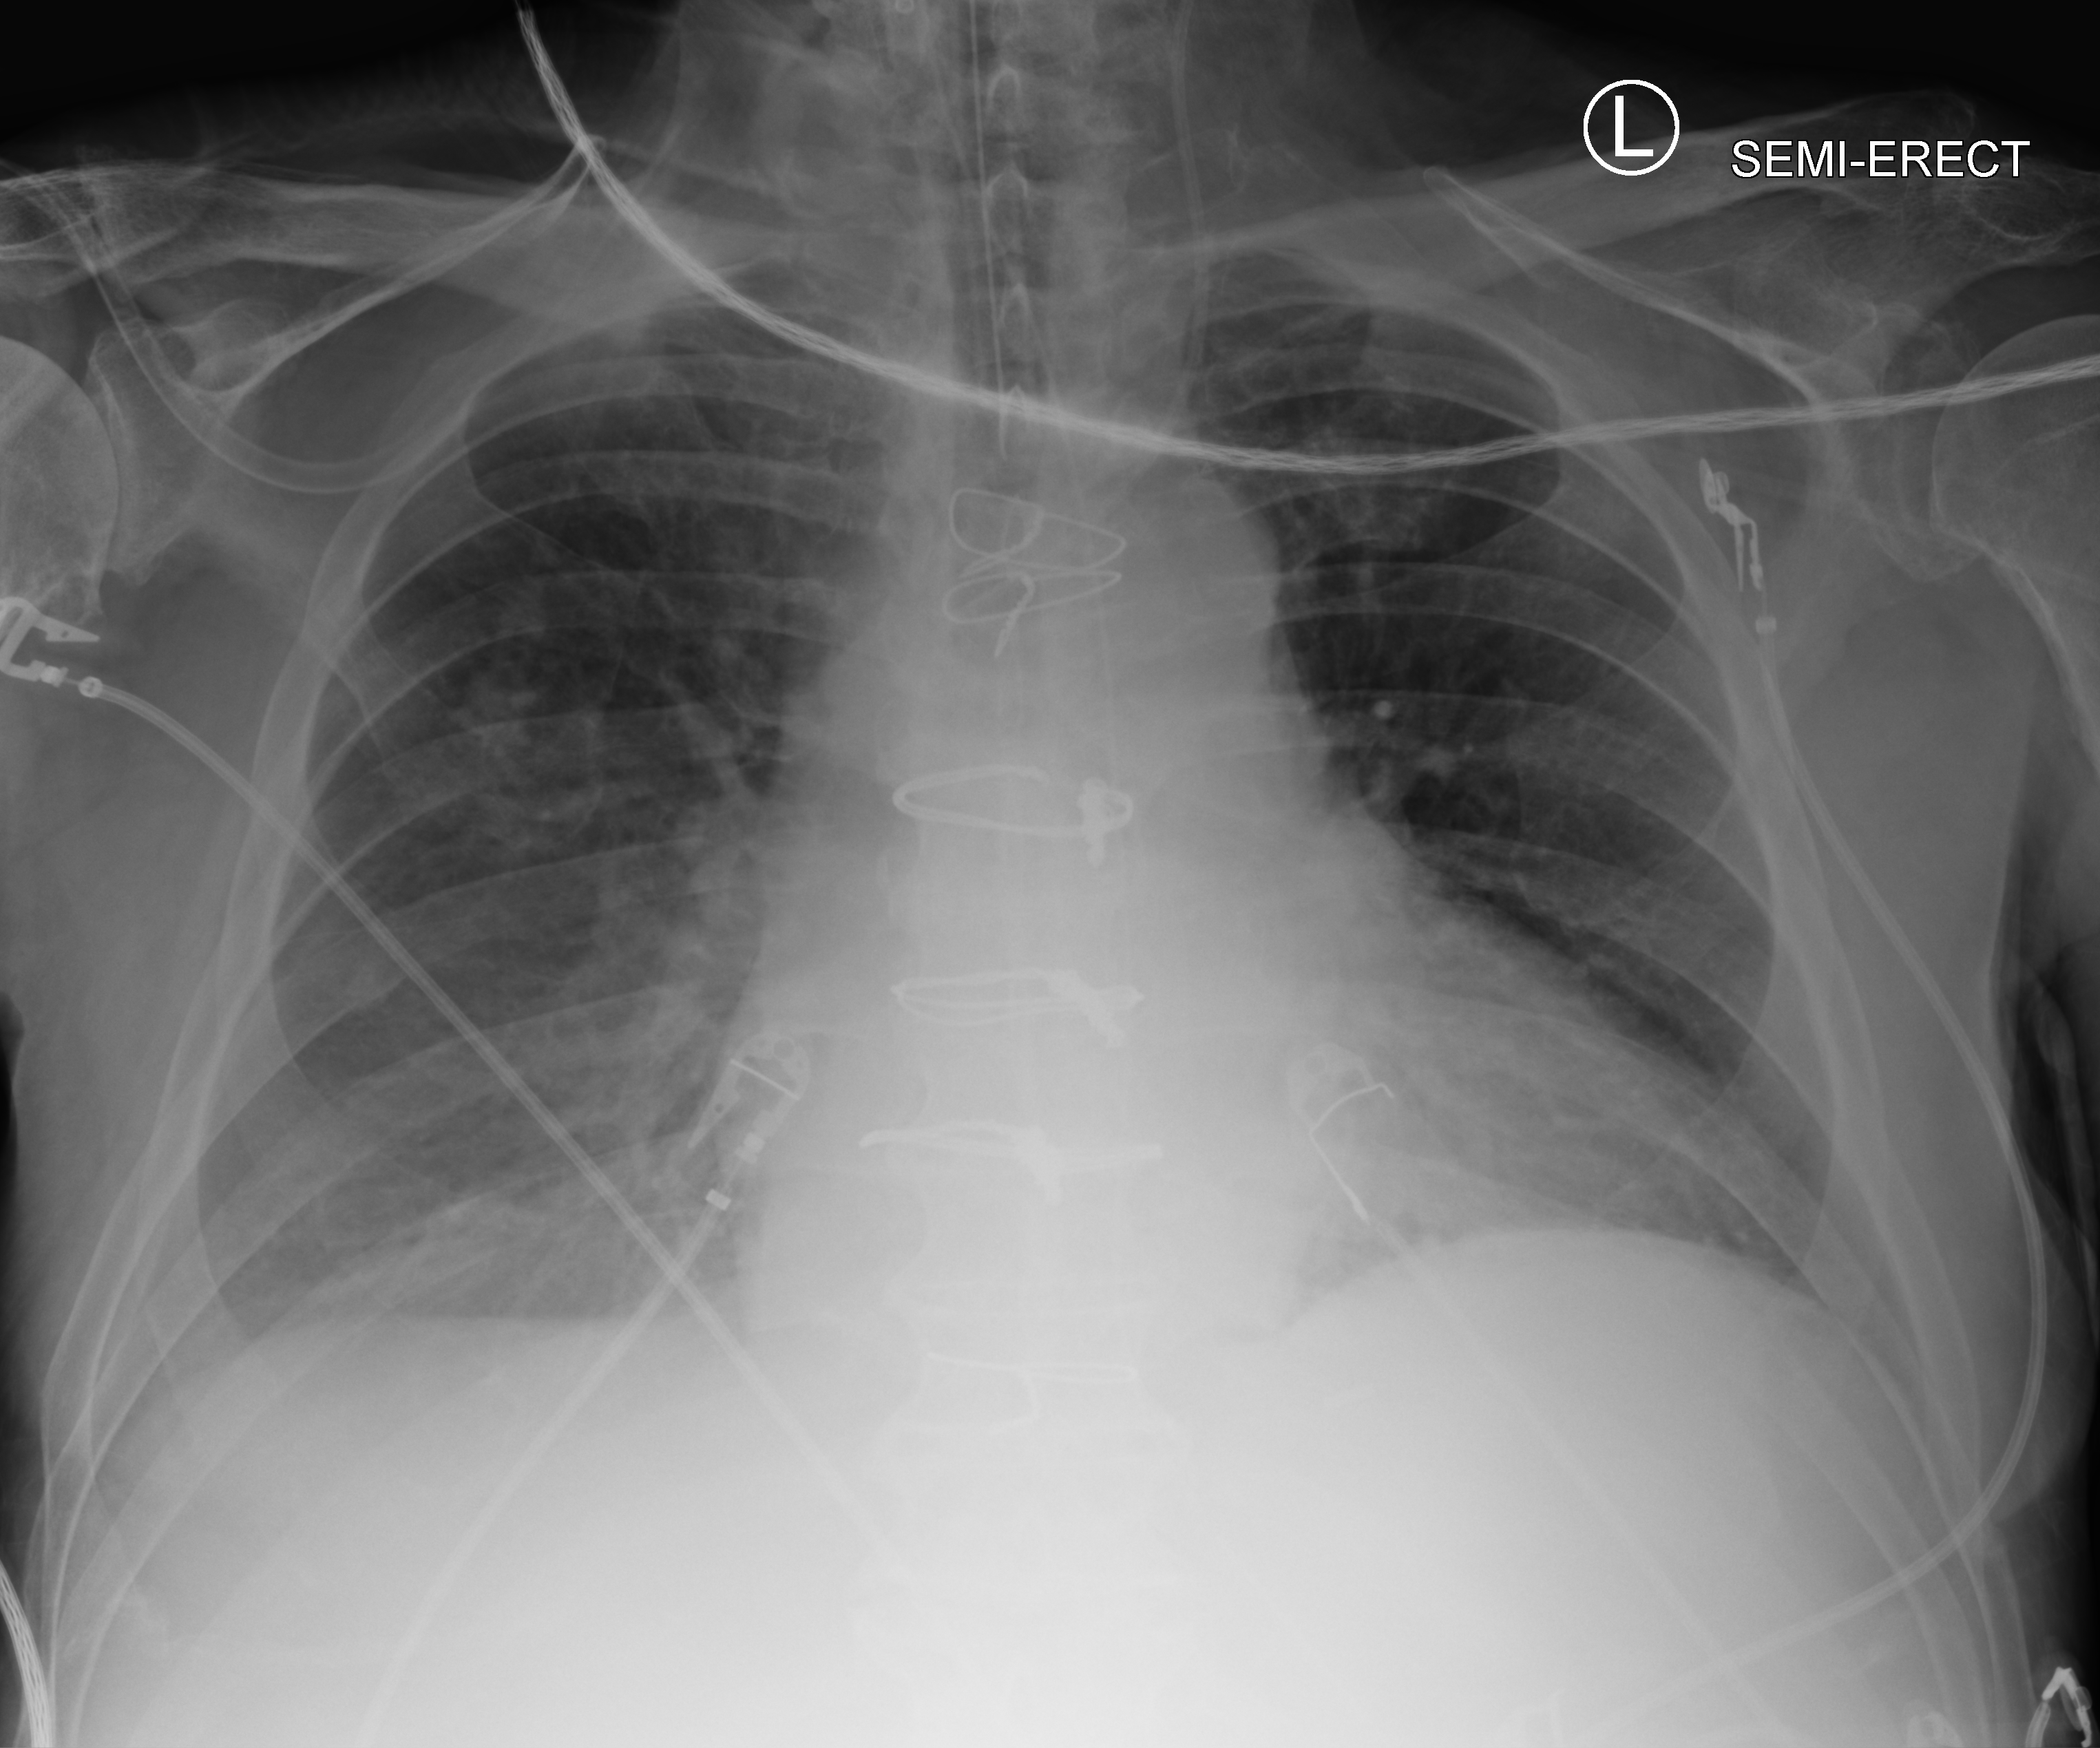
Chest X-ray (portable); anteroposterior (AP) projection. Patient hospitalised with COVID-19; male, aged 60–74 years.
Admission-level facts for this patient (not findings on this image; timing relative to this image not recorded): mechanically ventilated during this hospital stay: yes.